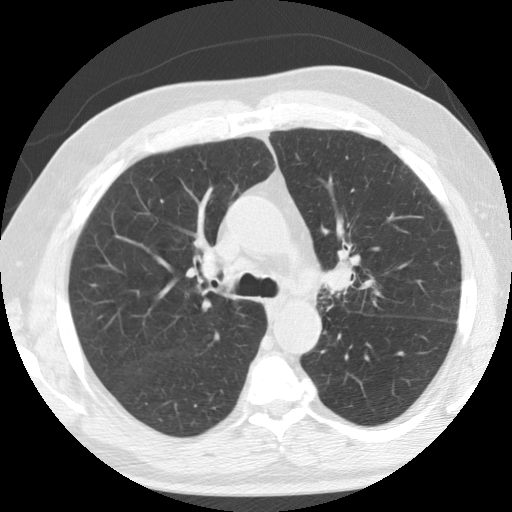
Low-dose screening chest CT, one axial slice. Position 88 of 133 along the scan axis. Reconstruction kernel STANDARD. 120 kVp. Lung window (W 1500 / L -600 HU). 2.5 mm slice thickness. 512 × 512 image matrix, field of view 342 × 342 mm.
Outlined on this slice (expert manual segmentation):
- lesion 1 (tumor, upper lobe of left lung): bounding box [x1, y1, x2, y2] px = [326, 261, 352, 290]